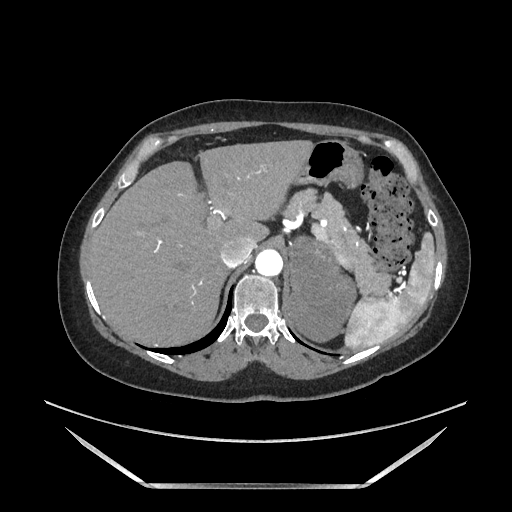
Contrast-enhanced abdominal CT, one axial slice. Position 135 of 205 along the scan axis. Soft-tissue window (W 400 / L 40 HU). 1.25 mm slice thickness. 512 × 512 image matrix, field of view 440 × 440 mm. Female patient. Case-level facts recorded for this patient, not image findings: diagnosis: adrenocortical carcinoma; tumour side: left adrenal; tumour size at pathology: 12.5 cm; Ki-67 index: 39 %; stage (as recorded): 3.
Annotated regions visible in this slice (semi-automatic segmentation, software-assisted and operator-edited):
- mass: bounding box <291,240,353,340> (left, top, right, bottom; pixels)